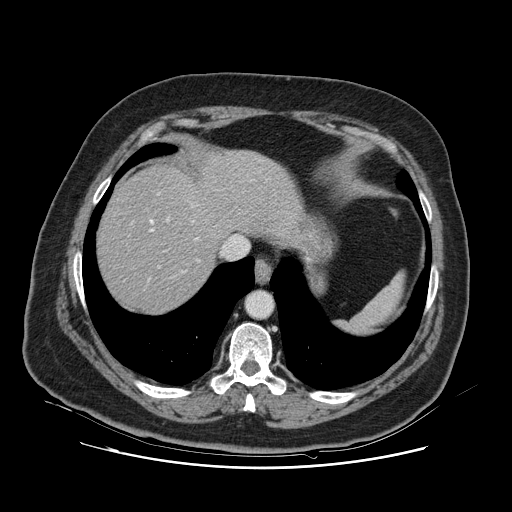
Contrast-enhanced abdominal CT, one axial slice; position 103 of 132 along the scan axis; 120 kVp; intravenous contrast given; soft-tissue window (W 400 / L 40 HU); 2.5 mm slice thickness; 512 × 512 image matrix, field of view 391 × 391 mm. Female patient, age 73 years. Case-level facts recorded for this patient, not image findings: diagnosis: colorectal cancer liver metastases, imaged before liver resection; multiple liver metastases: no; largest metastasis: 7 cm; disease in both lobes: no.
Structures marked on this image (outlined manually by an expert reader):
- hepatic veins: bounding box <131,205,199,274> (left, top, right, bottom; pixels)
- liver: <98,151,297,313>
- planned liver remnant (the part of the liver to remain after resection): <98,167,228,312>
- portal vein (with intrahepatic branches): <159,219,169,267>